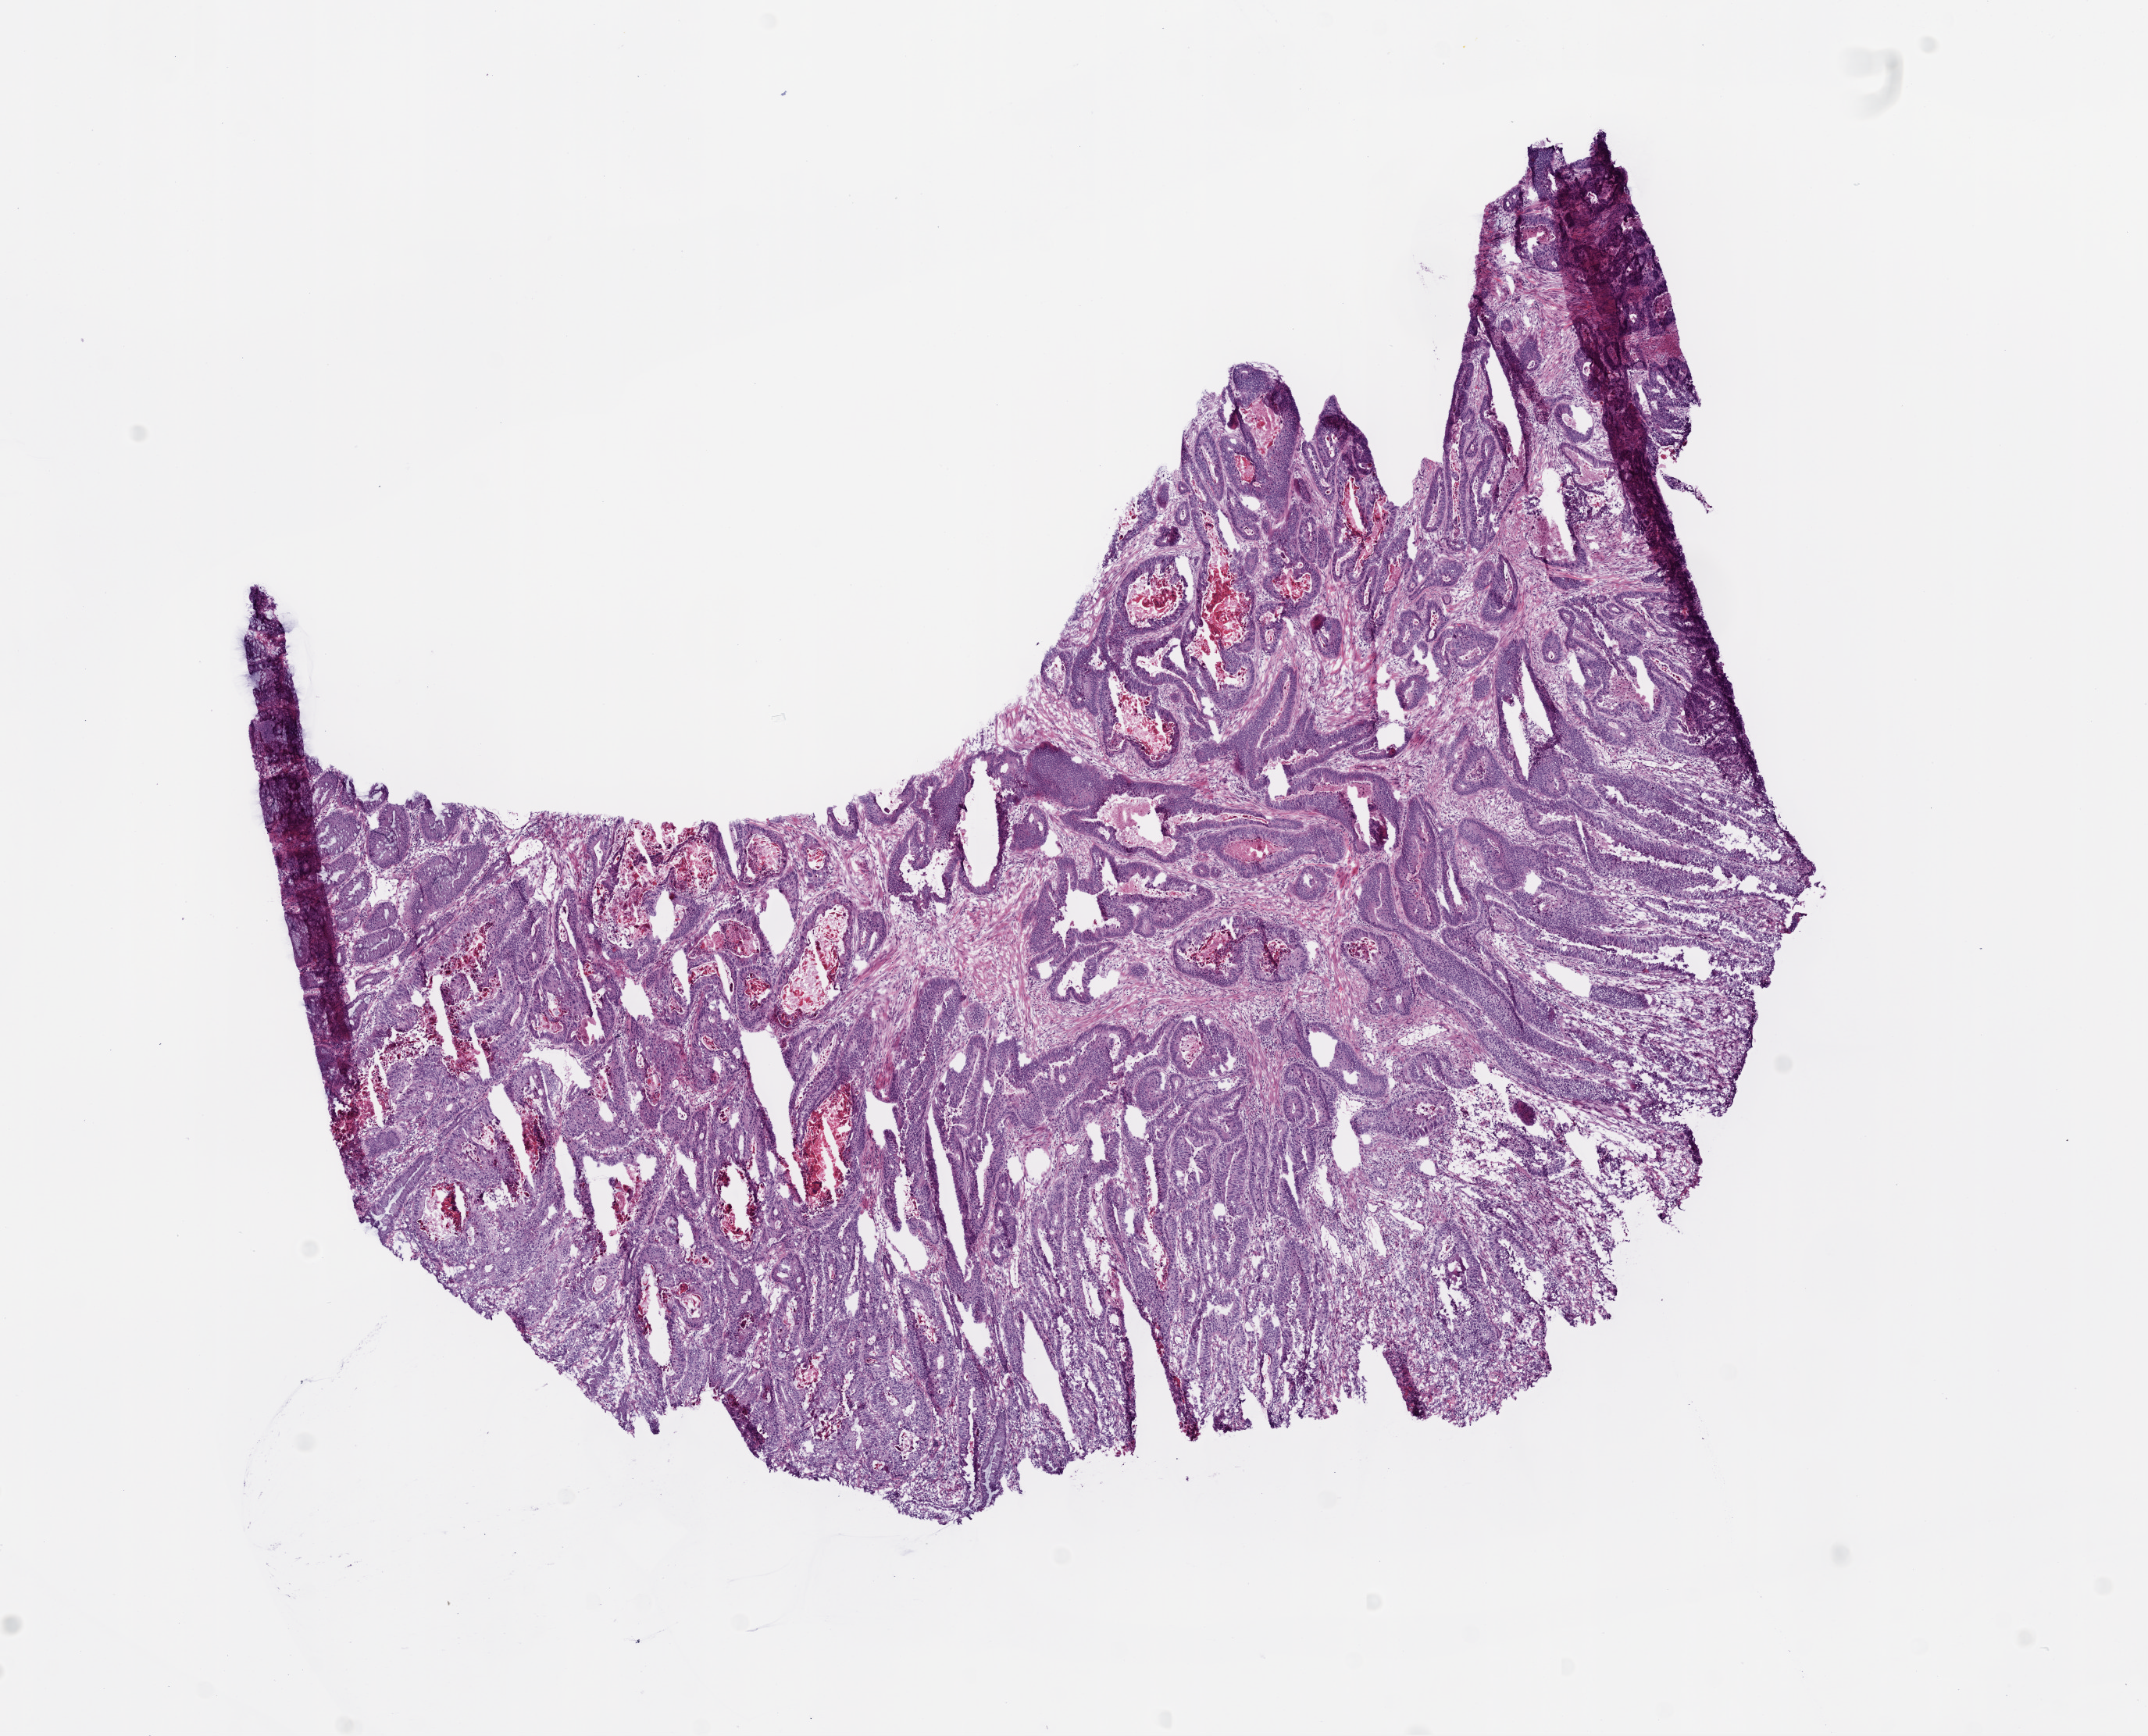
H&E-stained whole-slide image — low-resolution overview of the scanned area, about 11.0 x 8.9 mm (from a 20x scan), frozen section, sample: primary tumour, colon. Male patient; age at initial diagnosis 64 years. Composition of this section per pathologist review: tumour cells 73%, tumour nuclei 80%, normal cells 0%, stromal cells 15%, necrosis 12%.
* AJCC pathologic stage: II (5th edition)
* diagnosis: Adenocarcinoma, NOS
* lymph nodes positive (case pathology): 0 of 36 examined